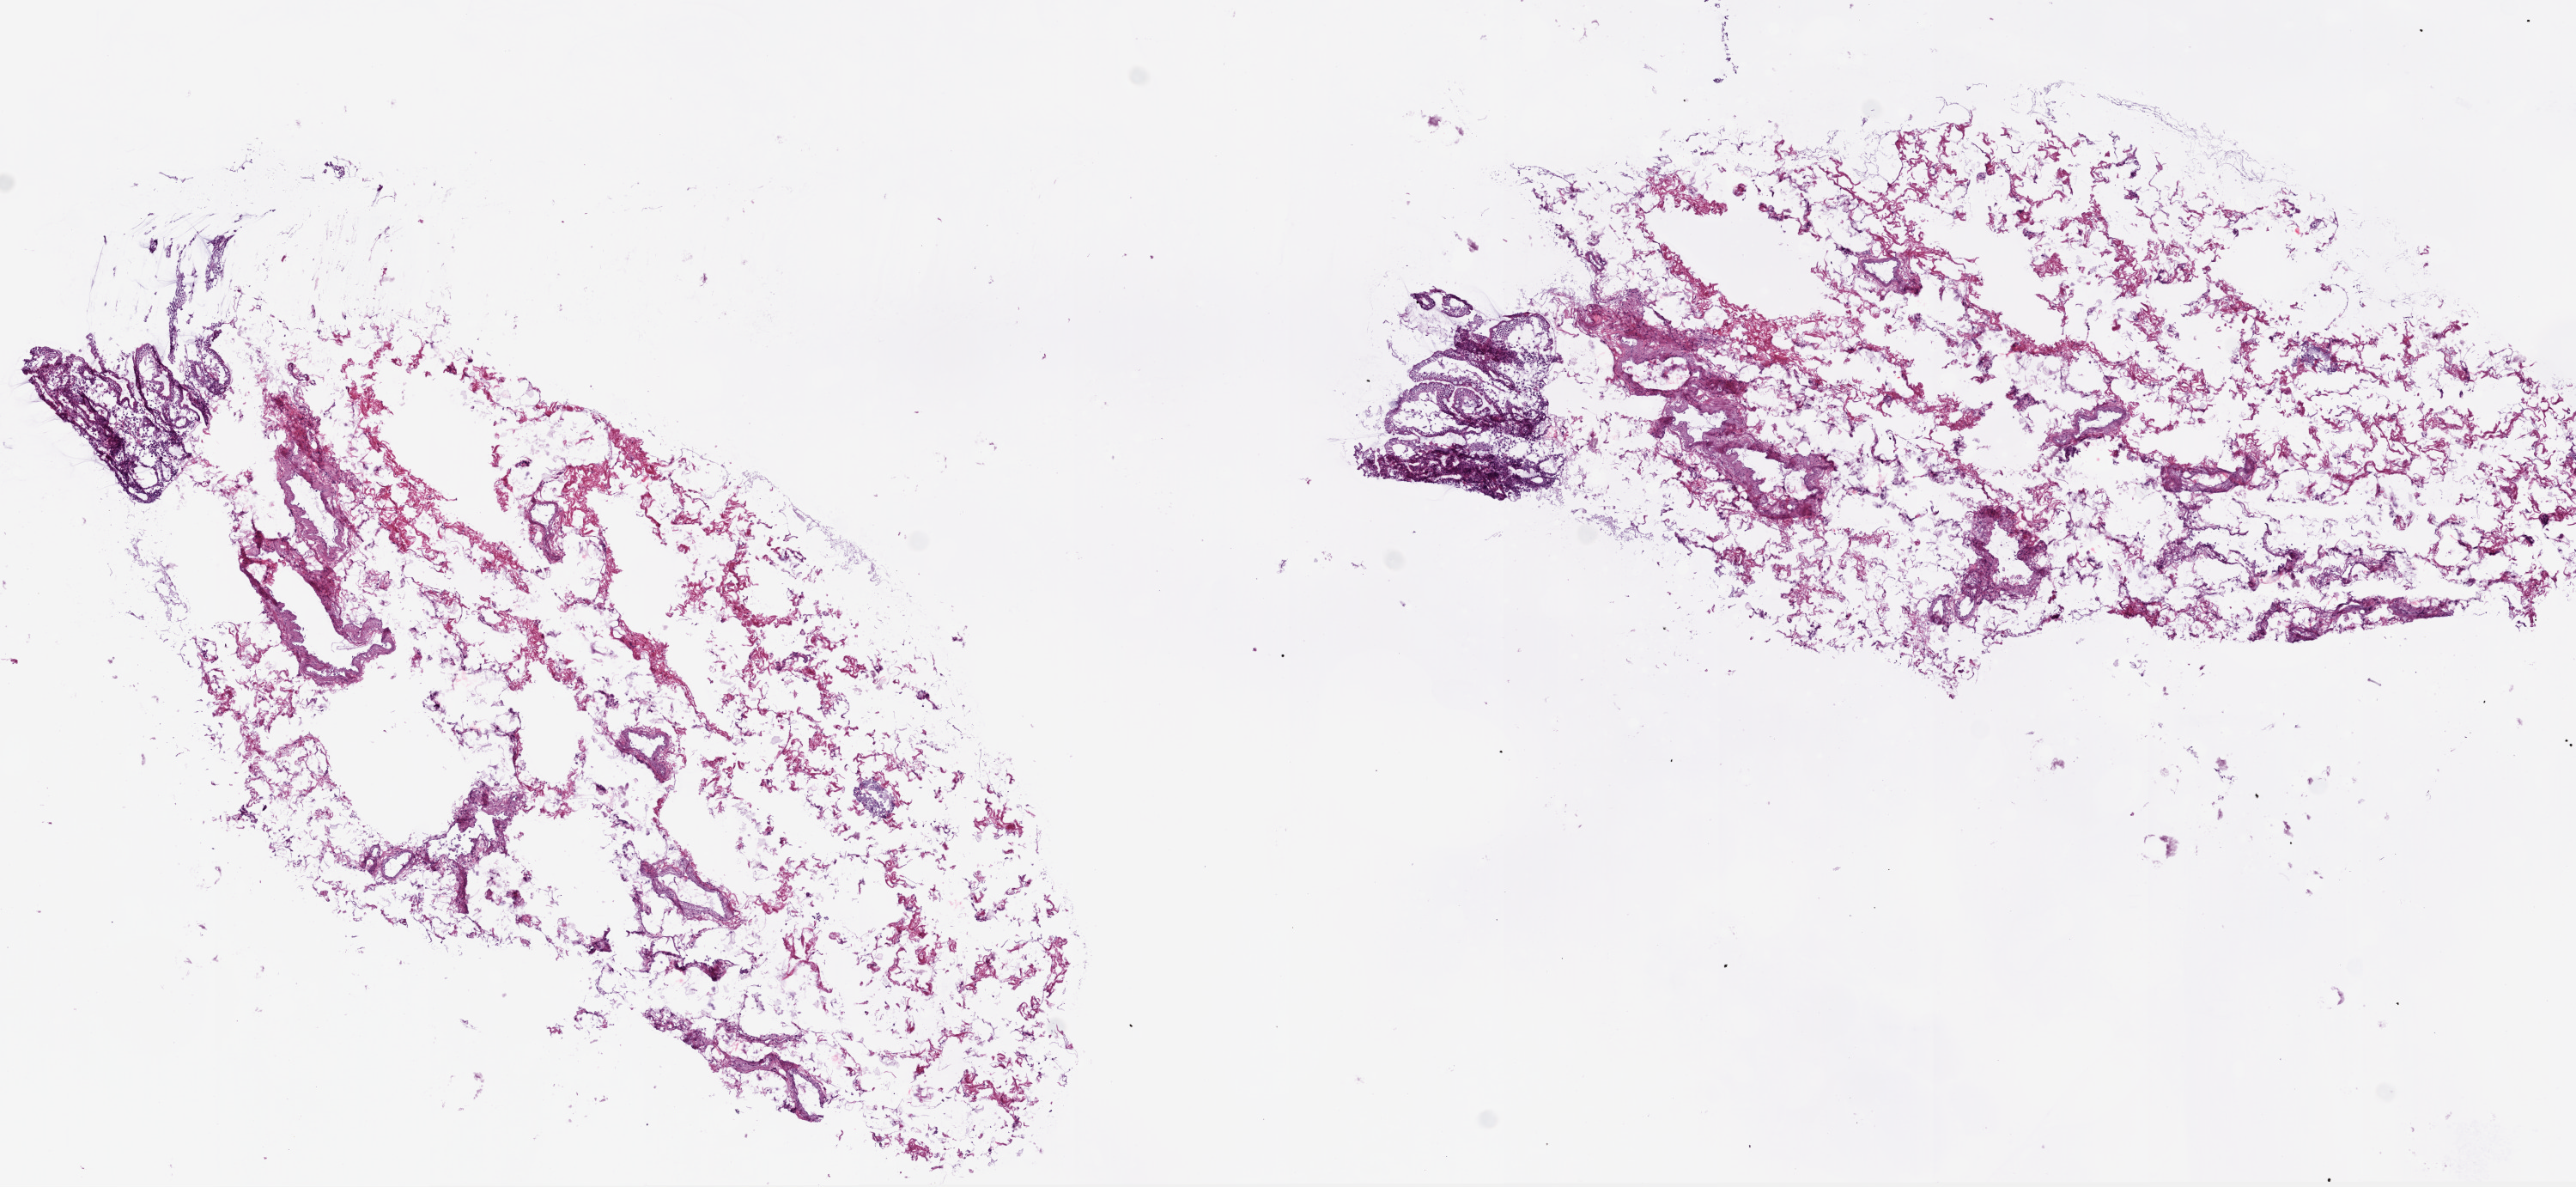
Digitized Hematoxylin and eosin (H&E) stained tissue section (whole slide), low-resolution overview of the scanned area, about 12.0 x 5.5 mm (acquisition: 20x scan). Frozen section from the top of the tissue portion. Solid tissue normal (non-tumour tissue) sample from the stomach. Patient: male, age at initial diagnosis 68 years.
• this section: solid tissue normal (non-tumour) sample from the same patient
• patient diagnosis: Adenocarcinoma, intestinal type (body of stomach)